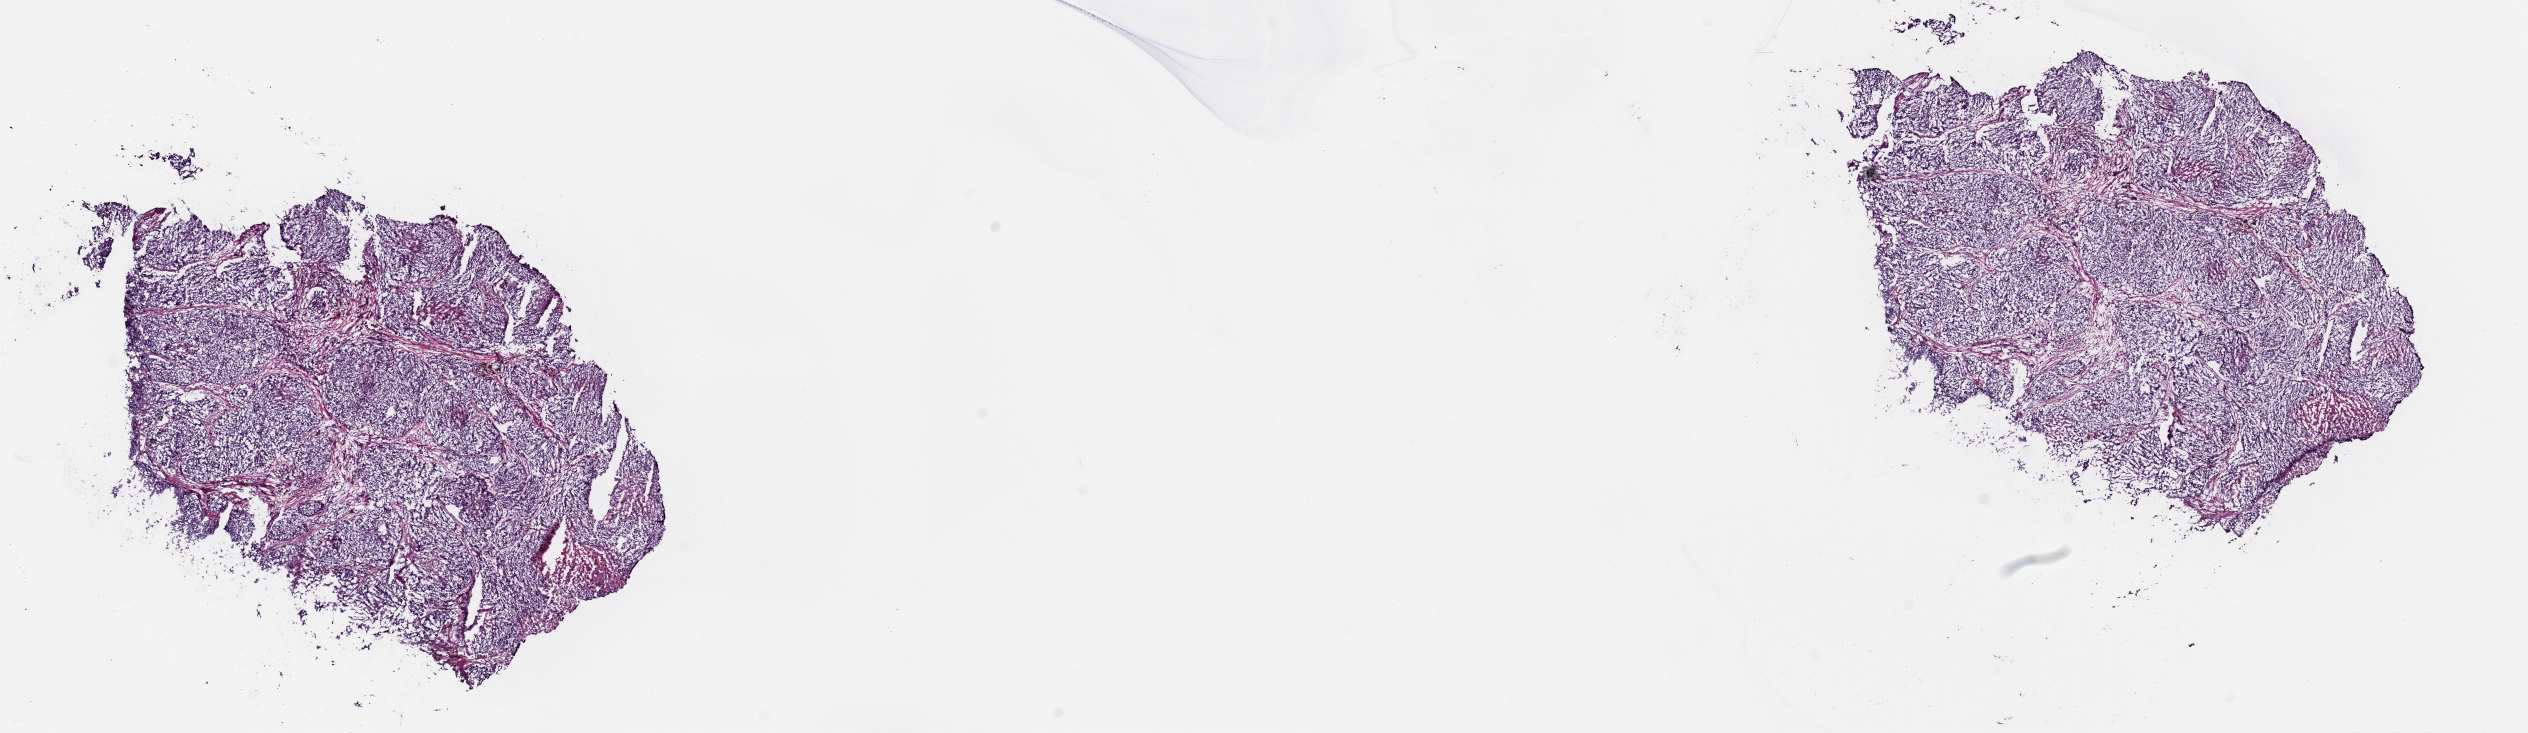
Digitized Hematoxylin and eosin (H&E) stained tissue section (whole slide) — shown as a low-resolution overview of the whole scanned area (about 20.0 x 5.8 mm, slide scanned at 40x); frozen section; metastatic tumour sample, sampled site not recorded. Male patient; age at initial diagnosis 79 years.
This section: metastatic tumour tissue. Patient diagnosis: Malignant melanoma, NOS.